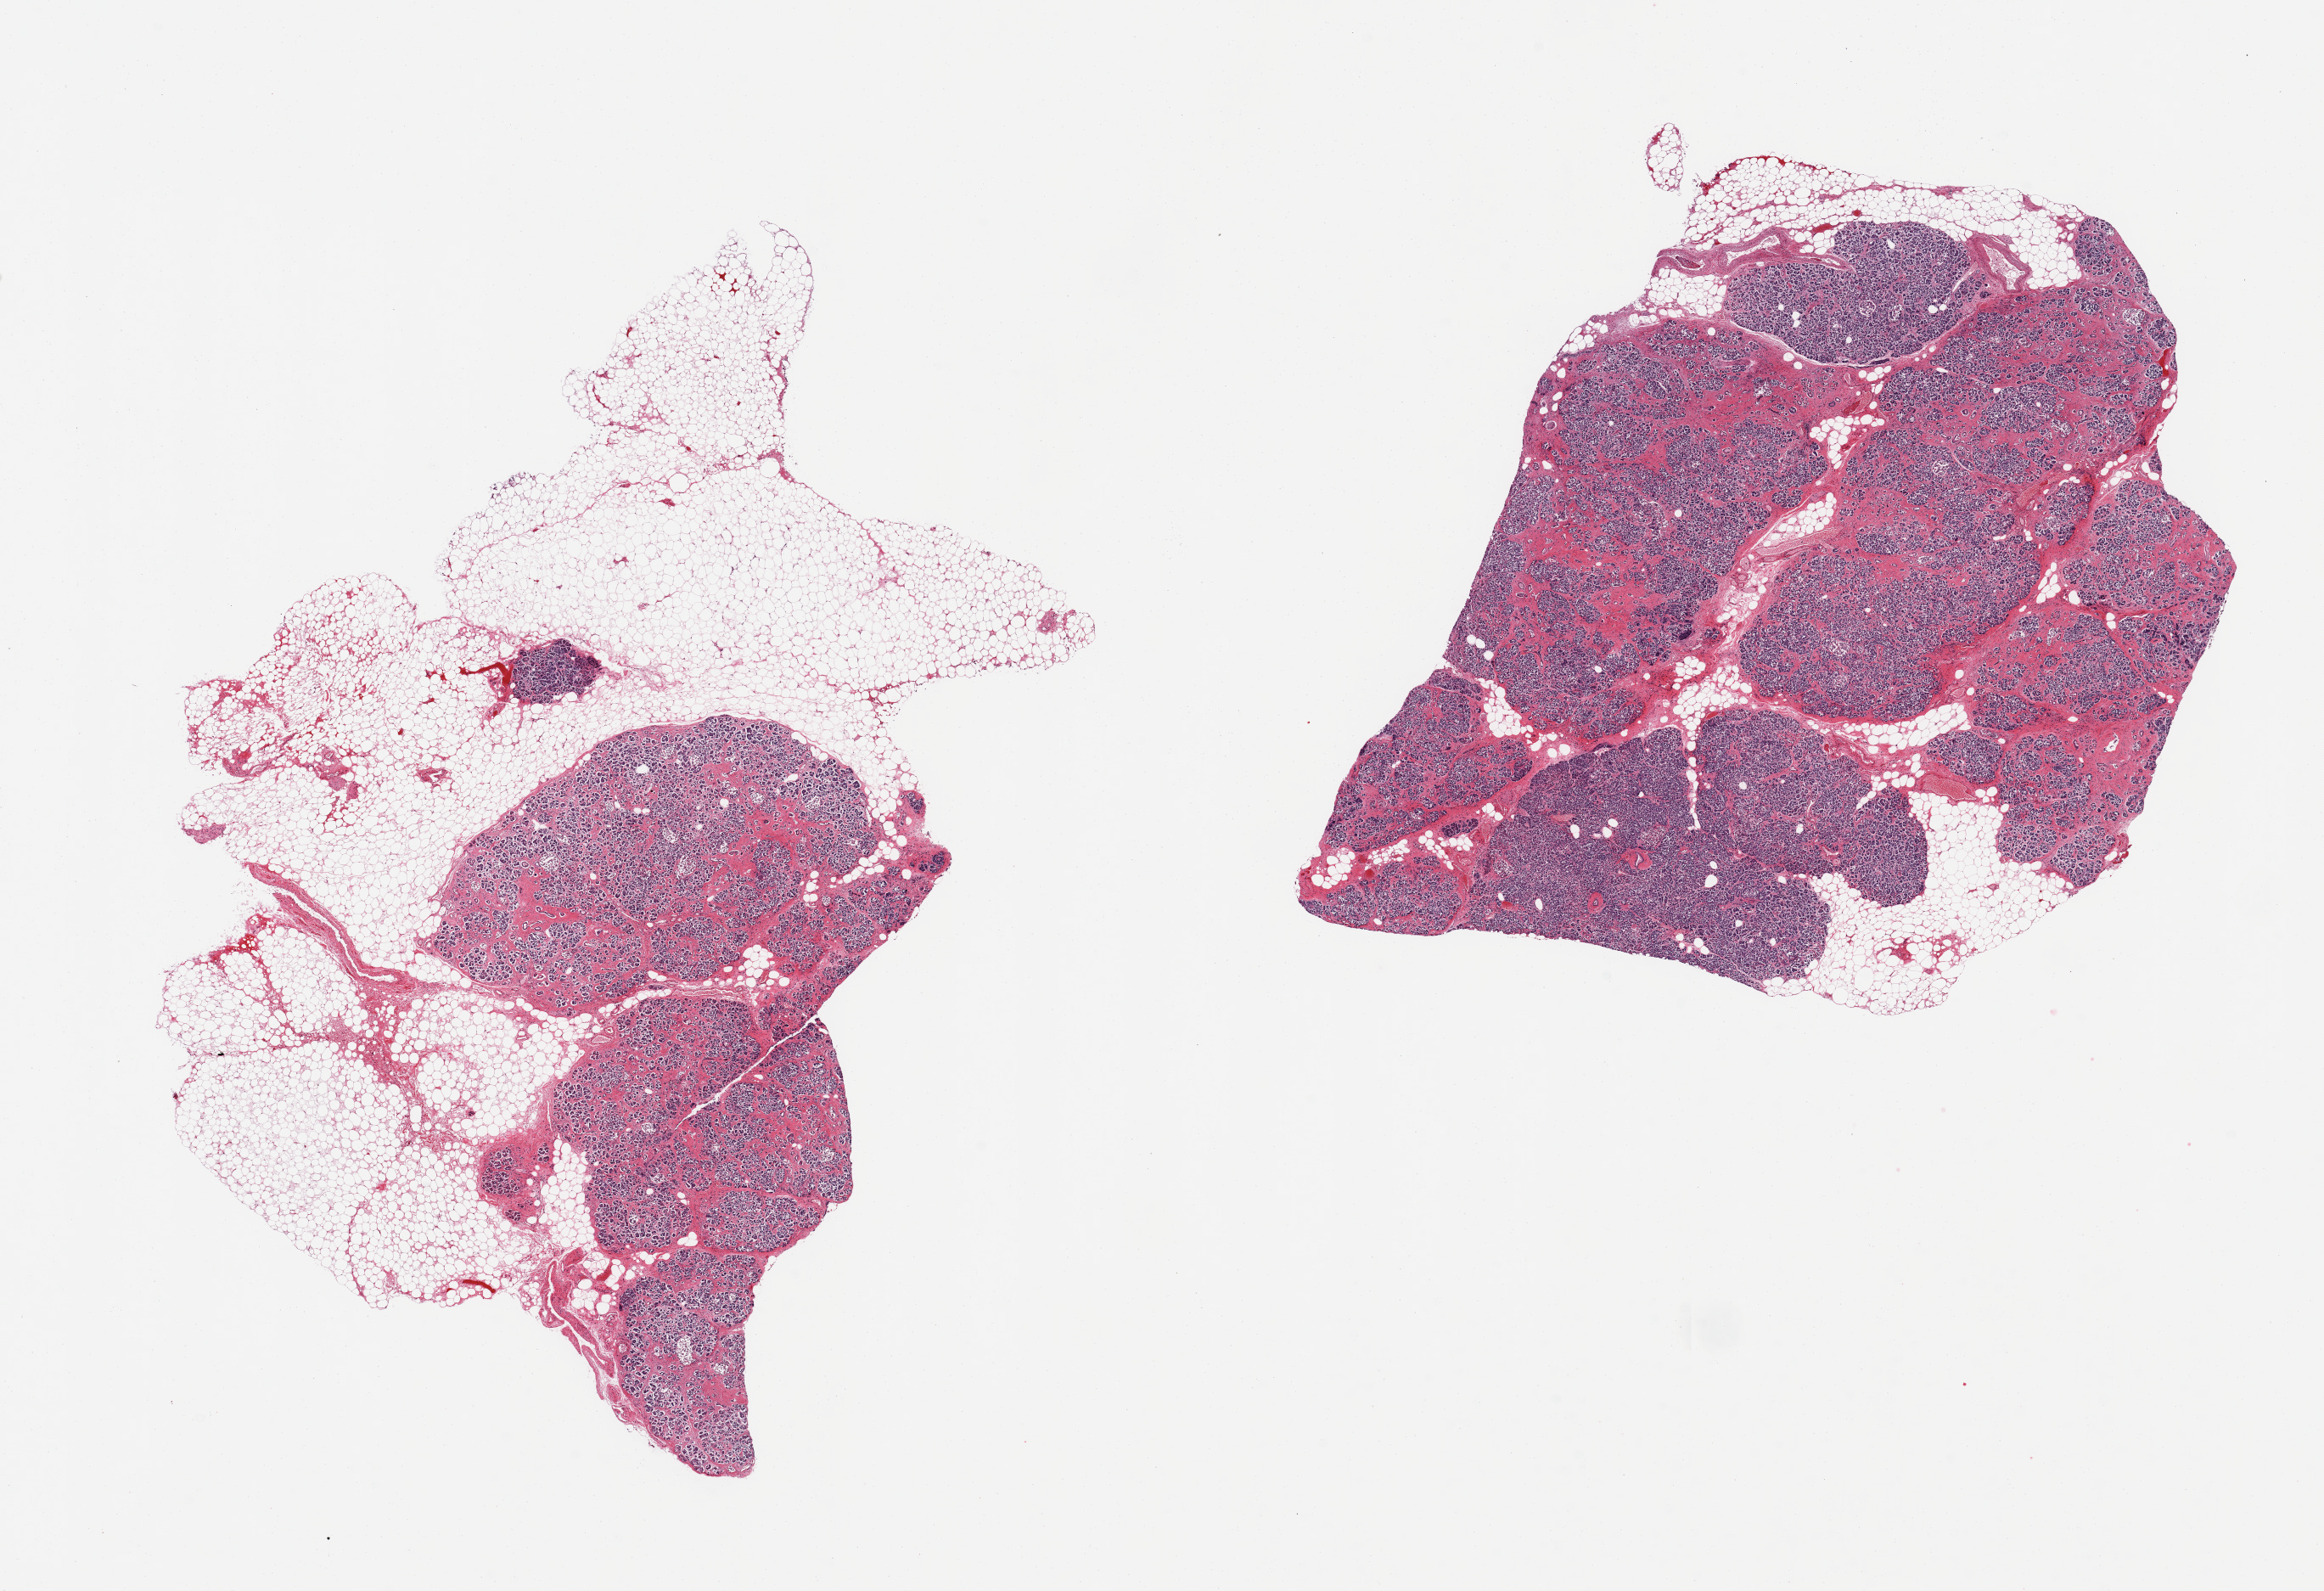
H&E whole-slide image, brightfield — low-resolution overview of the scanned area, about 21.7 x 14.8 mm (from a 20x scan). PAXgene-fixed, paraffin-embedded tissue. Sampled site (target tissue): pancreas. Donor tissue sample. Donor: female.
- pathologist's review note for this sample: 2 pieces; 50% and 10% fat content